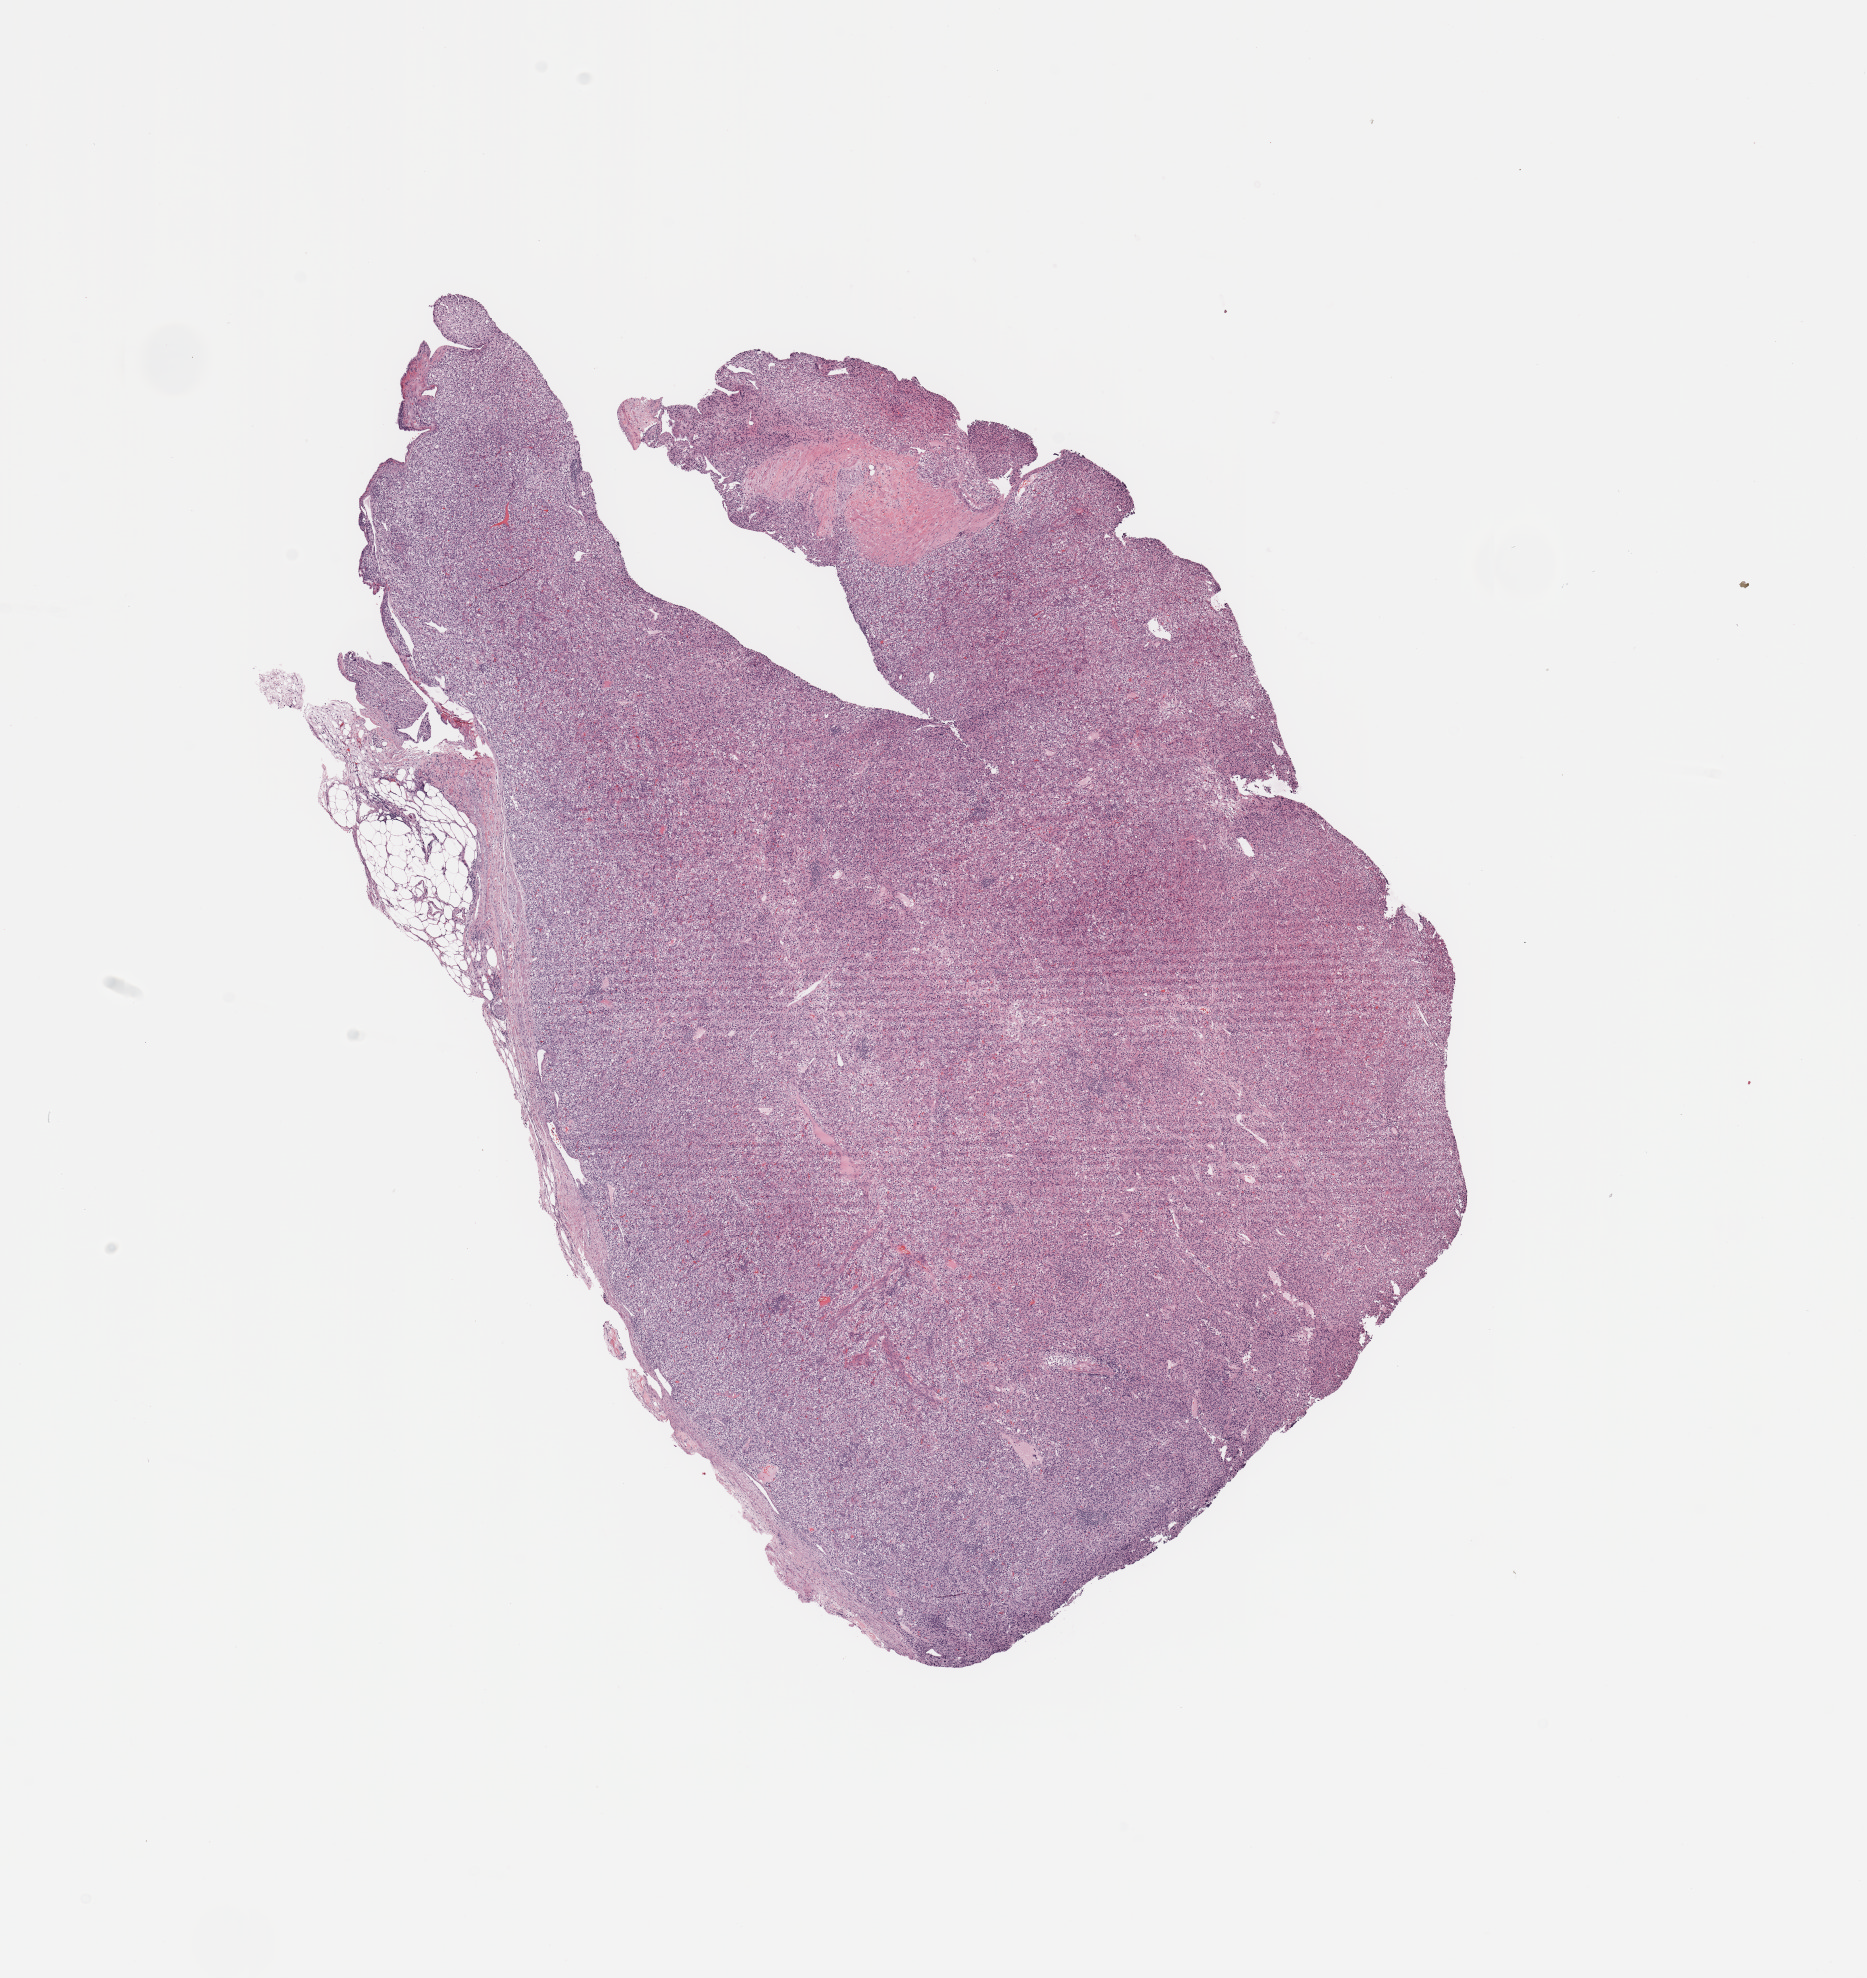
Whole-slide histology image, H&E-stained, shown as a low-resolution overview of the whole scanned area (about 14.8 x 15.6 mm, acquisition: 20x scan), tumour tissue sample, sampled site: kidney. Male, 68 y/o. Slide review estimates, as recorded: tumour nuclei 95%, necrosis 0%.
Histologic diagnosis: Renal cell carcinoma, NOS.